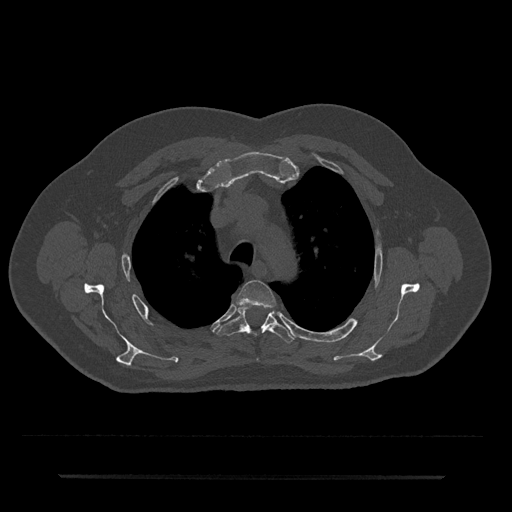
CT including the spine, one axial slice. Slice 543 of 797 in the series (ordered by position). Reconstruction kernel Br40s/3. 120 kVp. Bone window (W 1800 / L 400 HU). 0.5 mm slice thickness. 512 × 512 image matrix. Male patient, age 69 years. From the clinical record (not read from this slice): primary cancer: prostate.
Annotated regions visible in this slice (semi-automatic segmentation, software-assisted and operator-edited):
- T3 vertebra: bounding box <237,280,276,308> (left, top, right, bottom; pixels)
- T4 vertebra: <217,305,294,342>